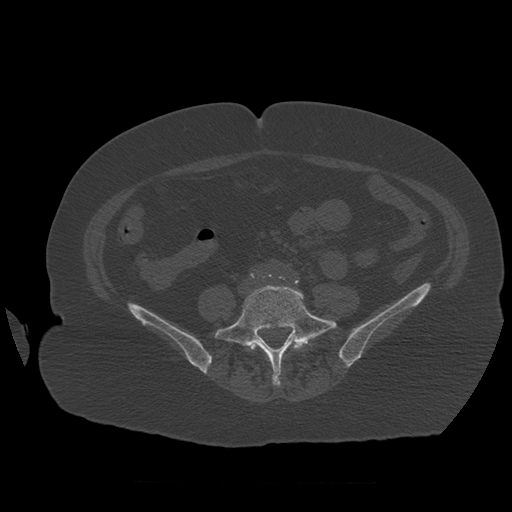
CT including the spine, one axial slice; position 187 of 399 along the scan axis; reconstruction kernel STANDARD; bone window (W 1800 / L 400 HU); 1.25 mm slice thickness; 512 × 512 image matrix. Patient age 81 years. From the clinical record (not read from this slice): primary cancer: renal; vertebrae with lytic lesions (as recorded): L1.
Outlined on this slice (semi-automatically segmented with operator editing):
- L4 vertebra: bounding box (x1, y1, x2, y2) in pixels: (251, 342, 304, 378)
- L5 vertebra: (215, 285, 337, 386)